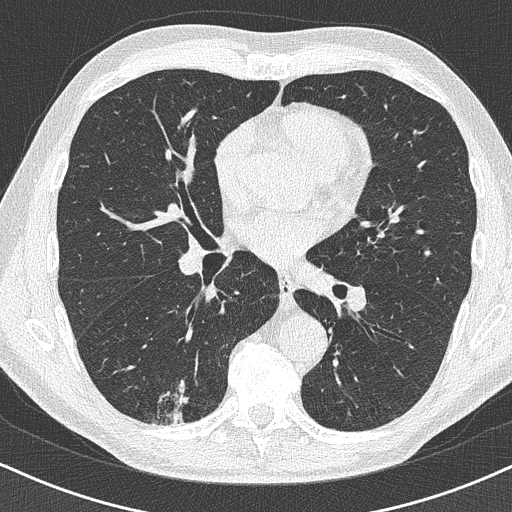
Low-dose screening chest CT, axial slice, baseline annual screen, lung window (W 1500 / L -600 HU), 1 mm slice thickness, slice 216 of 438 in the series, 512 × 512 image matrix, field of view 320 × 320 mm. Male participant, aged 63 years at enrolment.
• Expert reader's lesion annotation, box from (x=133, y=366) to (x=205, y=429) px.
• The exam's reader record, not a measurement of the box and not confirmed to be the same lesion: non-calcified nodule or mass ≥4 mm, right lower lobe, 16 × 13 mm, poorly defined margins.
• Lung cancer was diagnosed 74 days after this screen: adenocarcinoma, NOS, right lower lobe, moderately differentiated (G2), stage IA (AJCC 6th edition), 20 mm at pathology.